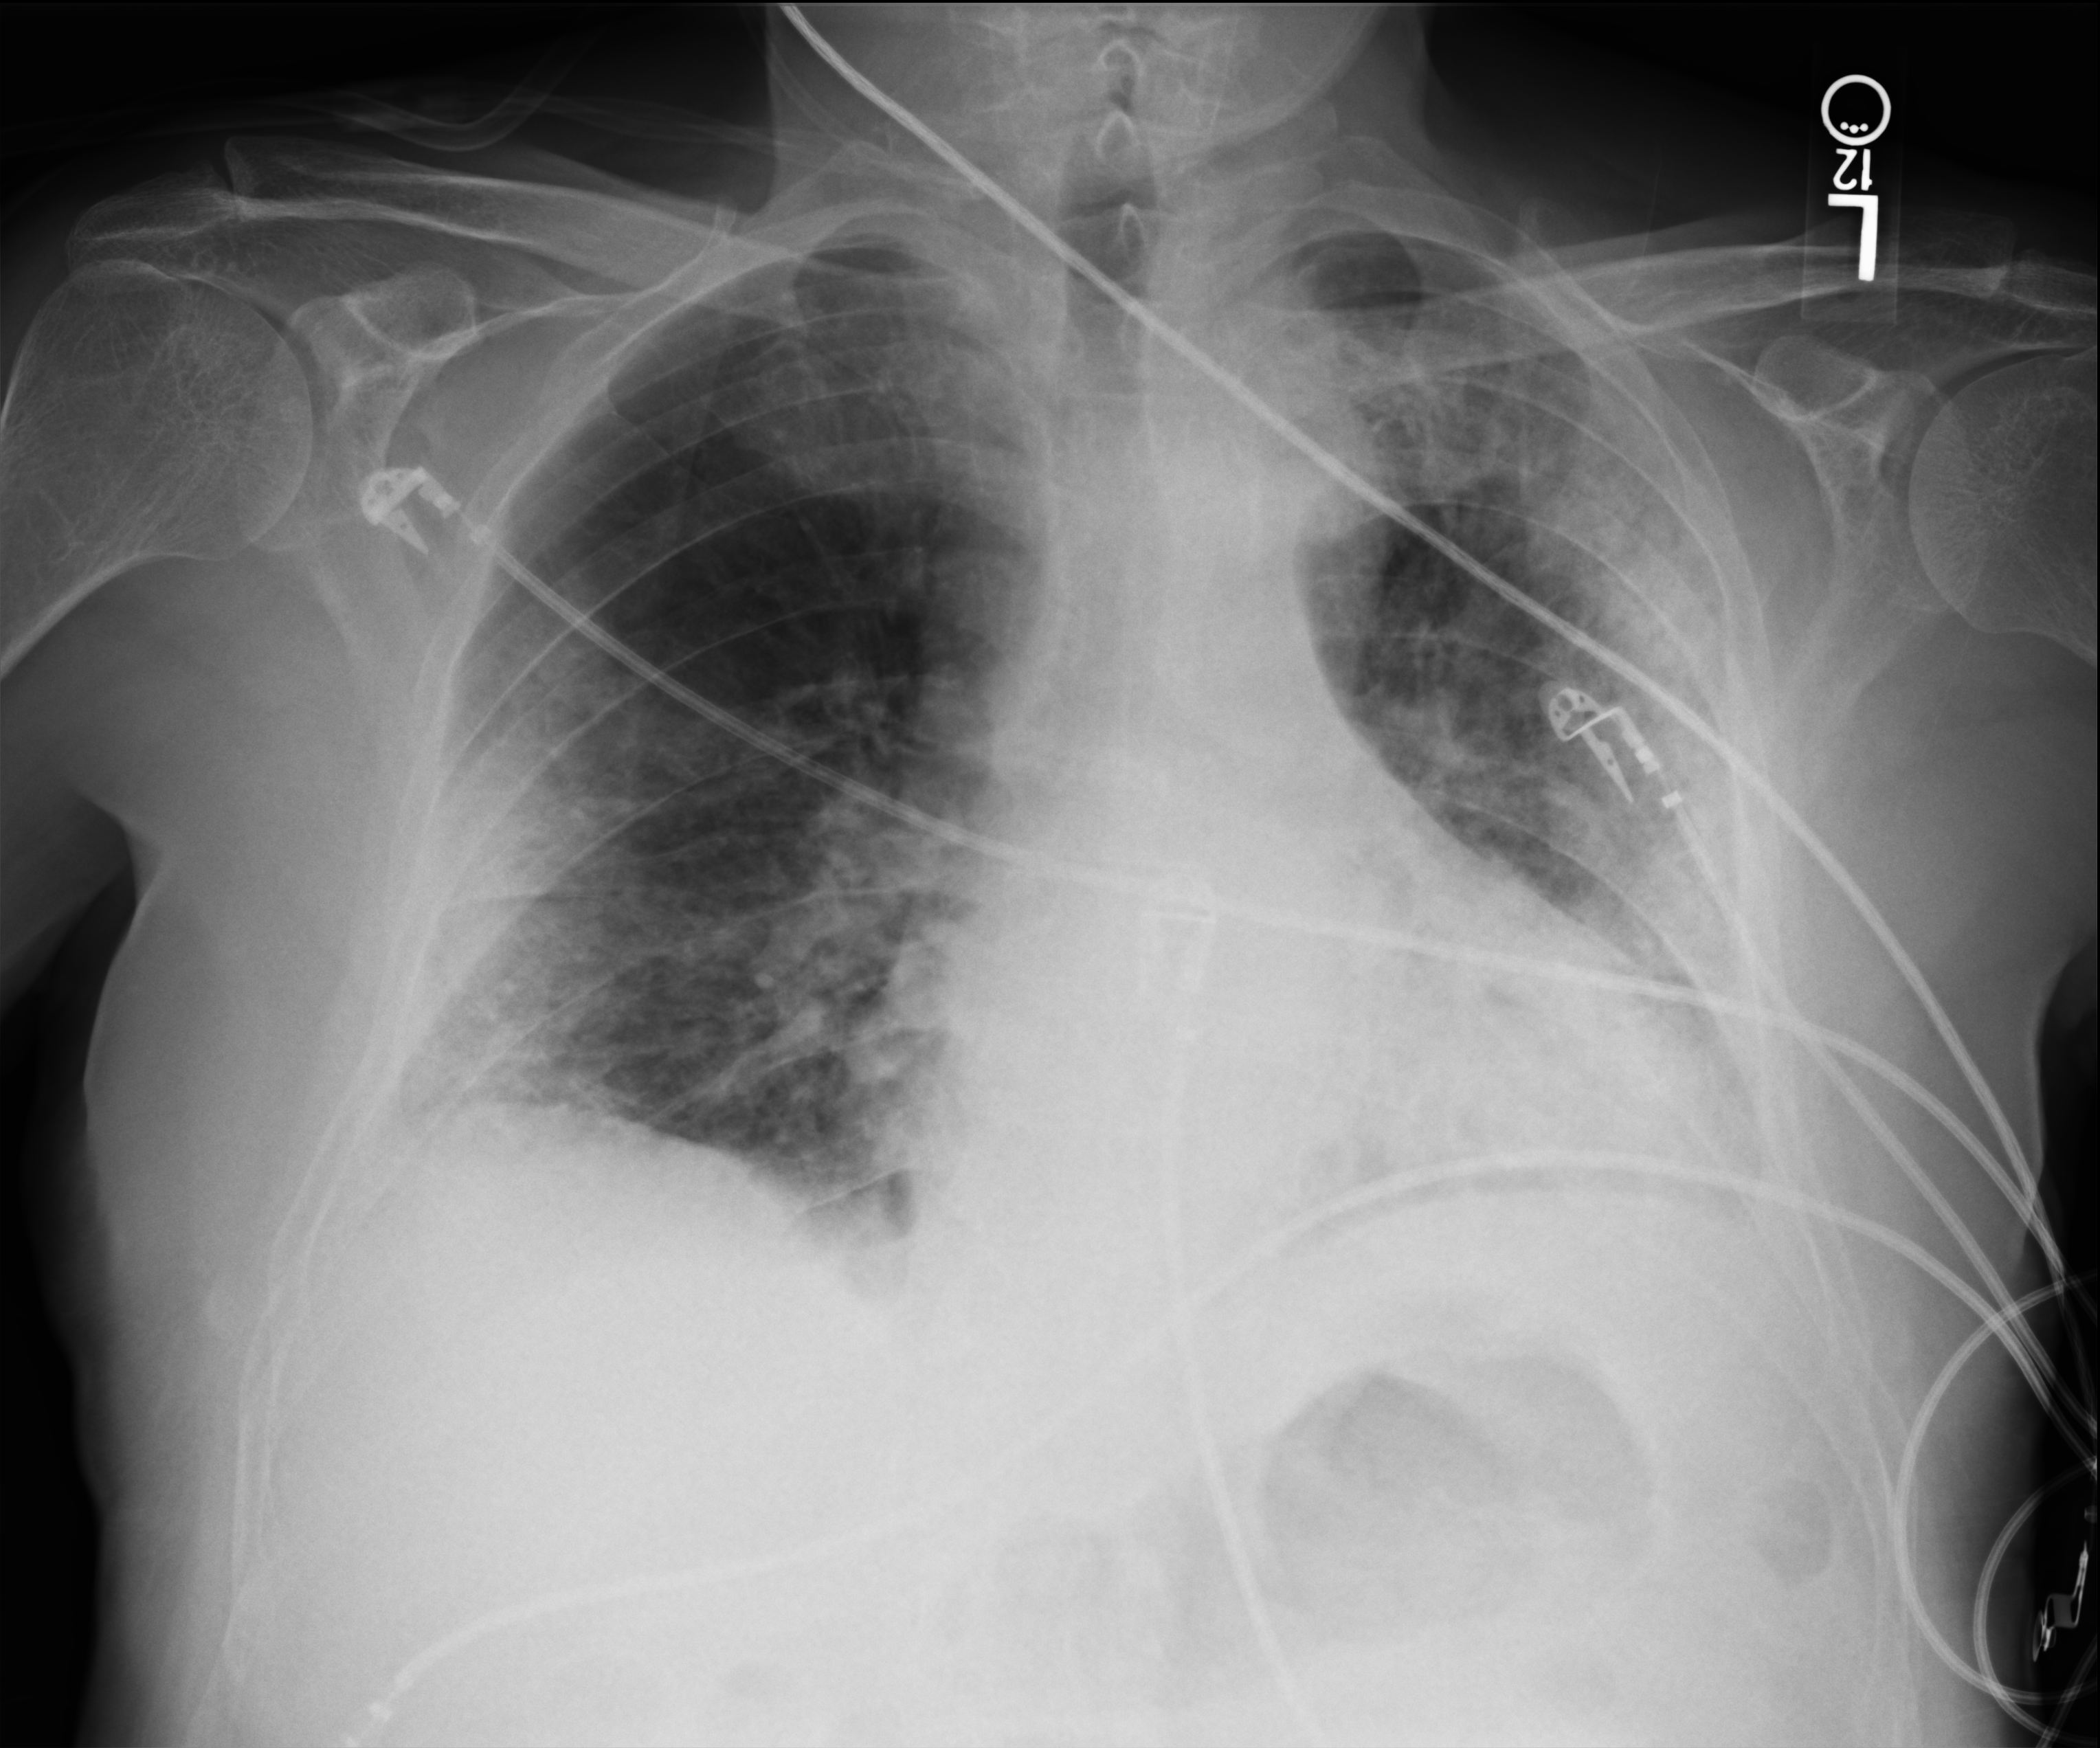
Portable chest radiograph; anteroposterior (AP) projection. Male patient hospitalised with COVID-19, age 60–74 years.
Hospital-stay facts (about this admission, not read from this image; timing relative to this image not recorded): admitted to intensive care during this hospital stay: no.